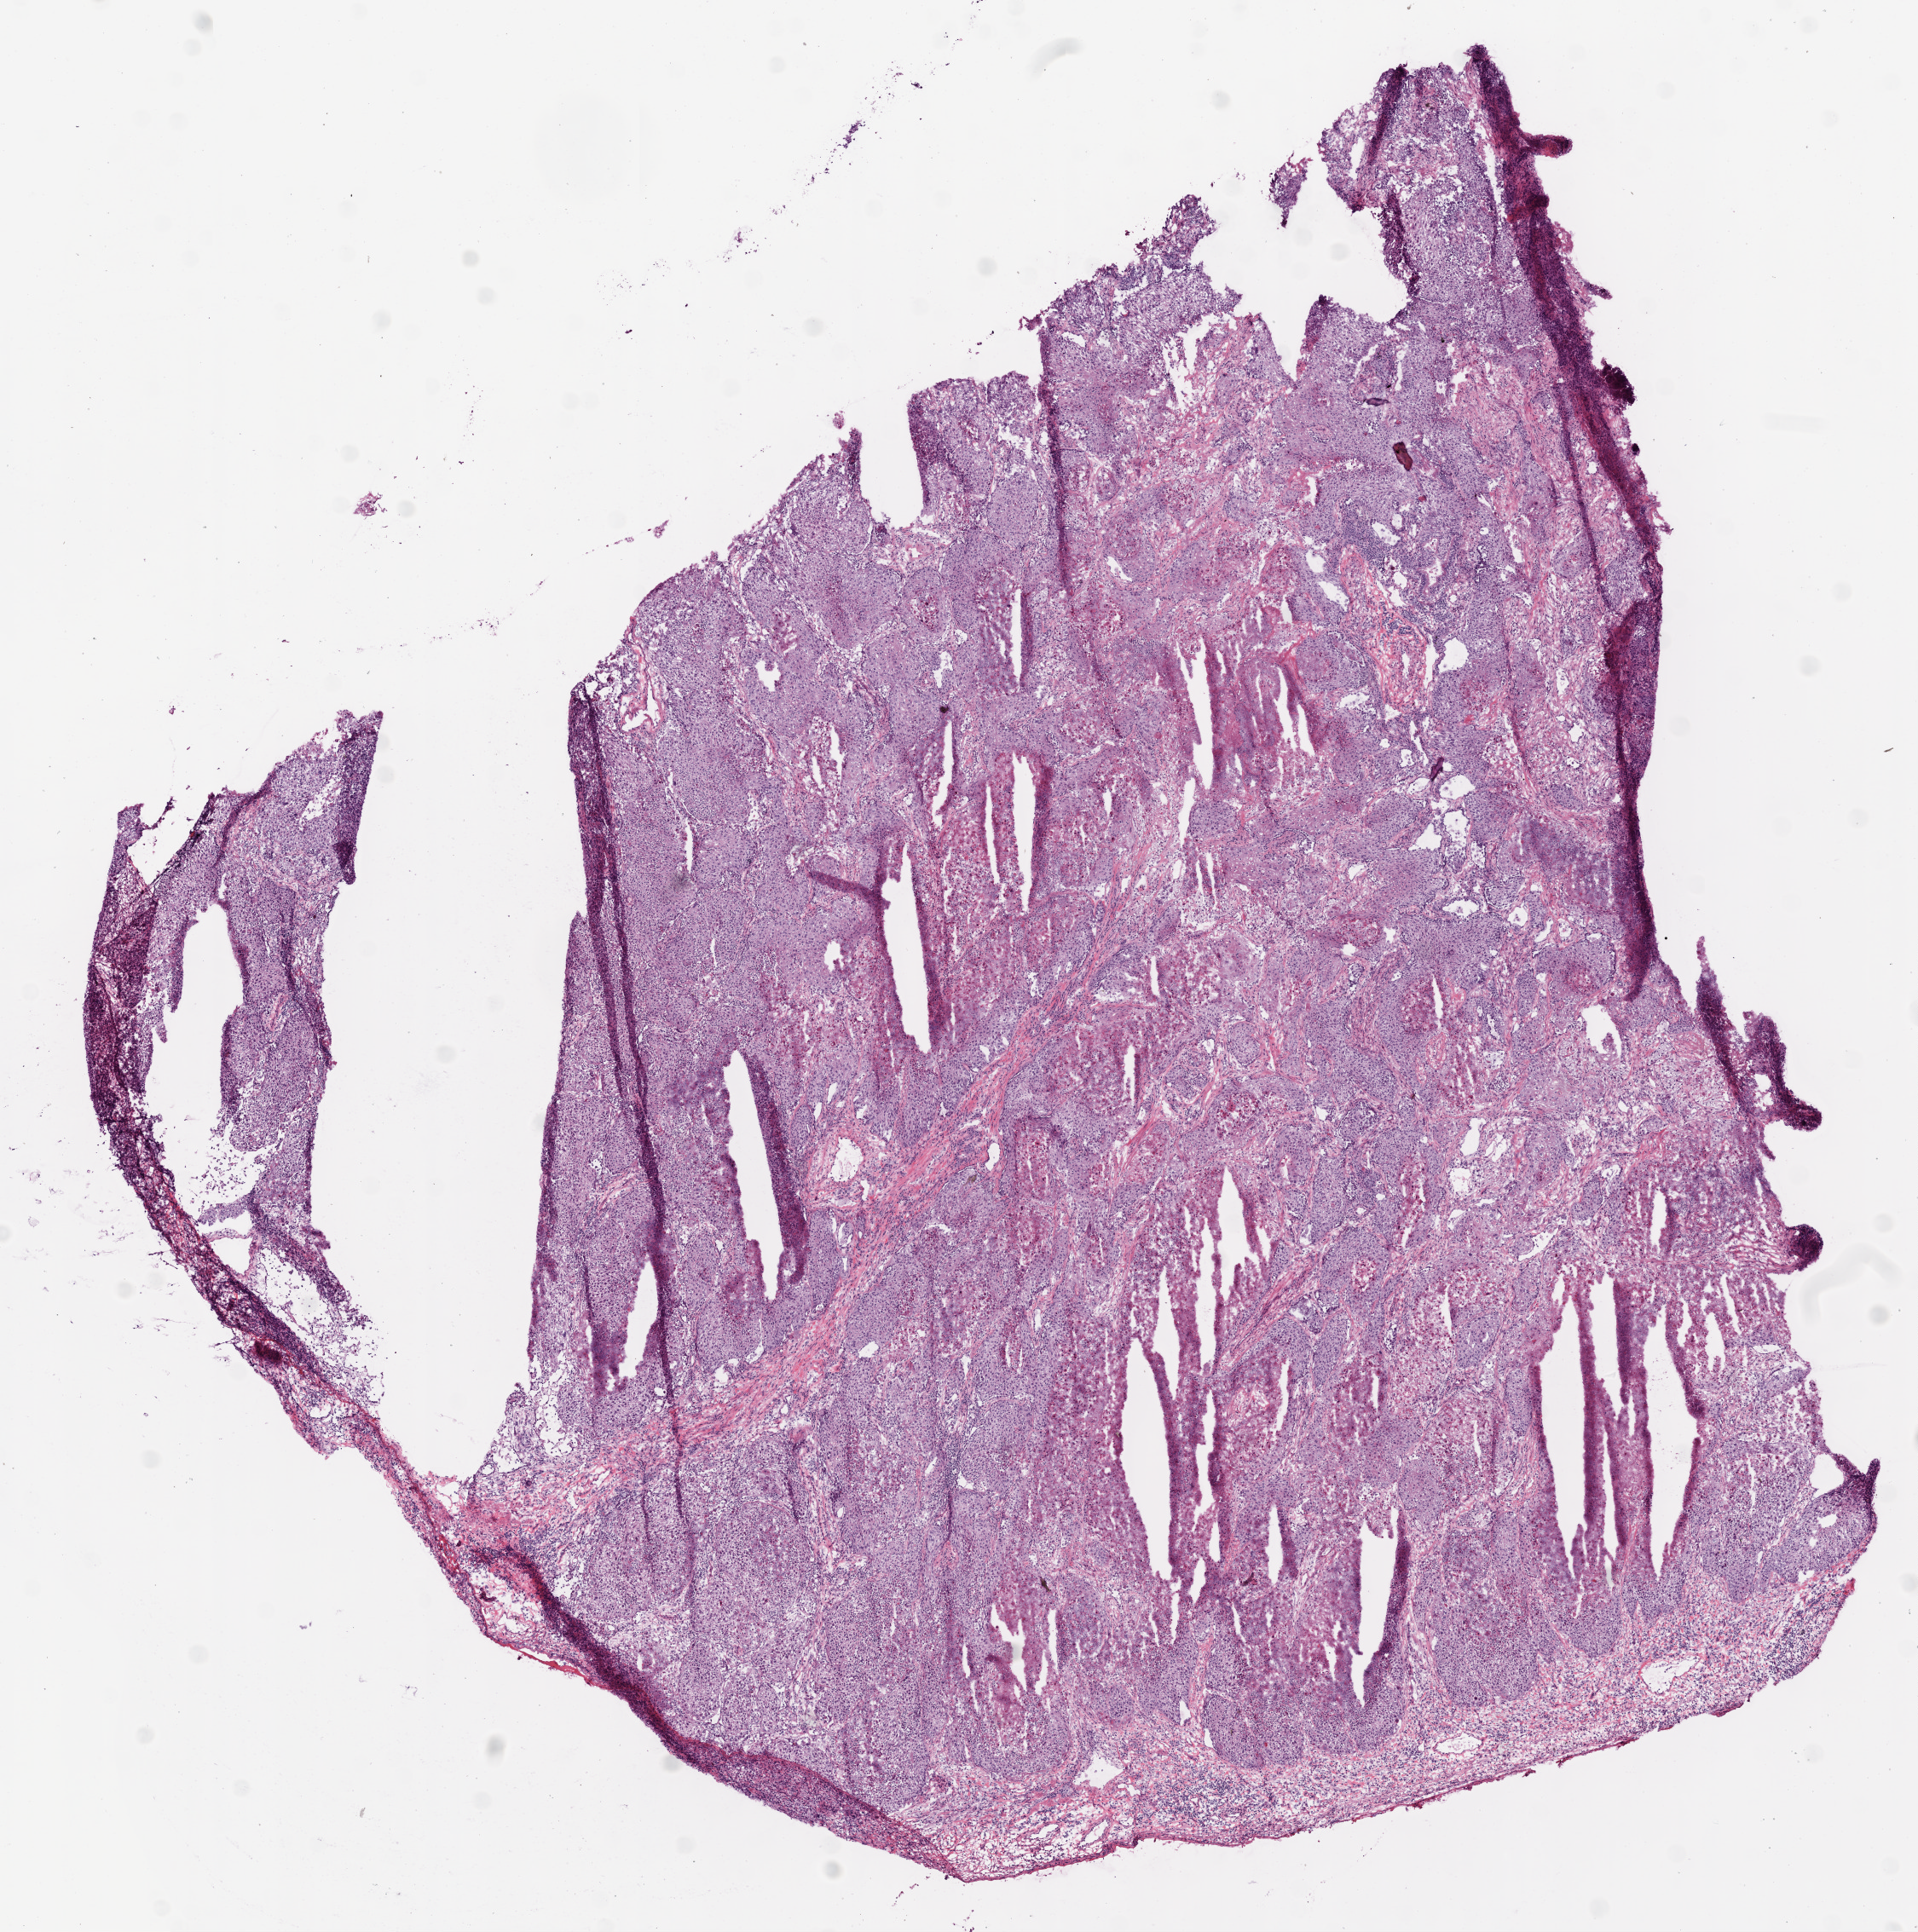
Digitized H&E-stained tissue section (whole slide), shown as a low-resolution overview of the whole scanned area (about 9.0 x 9.1 mm, acquisition: 20x scan). Frozen section. Primary tumour sample from the lung. Female patient; age at initial diagnosis 68 years. Pathologist review of this section (percent, as recorded): tumour cells 62%, tumour nuclei 90%, normal cells 8%, stromal cells 5%, necrosis 25%.
- AJCC pathologic stage: IIIB (6th edition)
- TNM: T2 N3 M0
- diagnosis: Squamous cell carcinoma, NOS (lower lobe, lung)